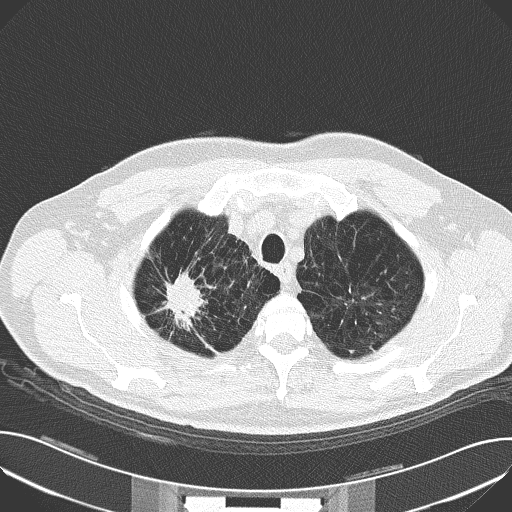
Low-dose screening chest CT, axial slice; baseline annual screen; lung window (W 1500 / L -600 HU); lung (sharp) reconstruction kernel (B50f); slice 22 of 159 in the series; 512 × 512 image matrix, field of view 380 × 380 mm. Male, age 59 years at enrolment.
• Expert-annotated lung lesion, box from (x=154, y=260) to (x=219, y=330) px.
• The screening reader recorded 4 non-calcified nodules or masses ≥4 mm on this exam (right upper lobe, left upper lobe, right upper lobe, left upper lobe); which of them this box marks is not recorded.
• Official screen result: positive, change unspecified: nodule(s) >= 4 mm or enlarging nodule(s), mass(es), or other non-specific abnormalities suspicious for lung cancer.